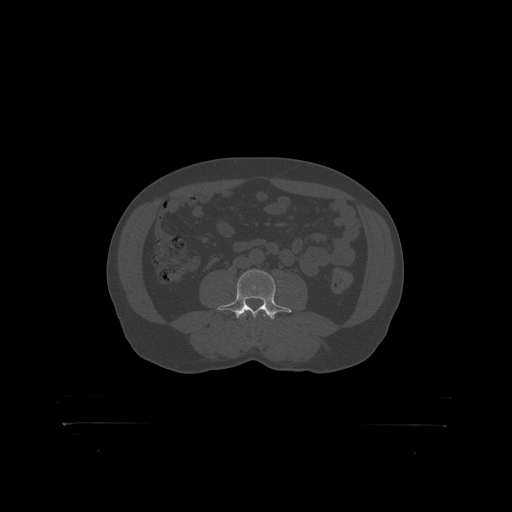
CT including the spine, one axial slice. Position 242 of 399 along the scan axis. Reconstruction kernel STANDARD. Bone window (W 1800 / L 400 HU). 1.25 mm slice thickness. 512 × 512 image matrix, field of view 650 × 650 mm. Male patient, age 46 years. Case-level facts recorded for this patient, not image findings: primary cancer: skin.
Outlined on this slice (semi-automatically segmented with operator editing):
- L3 vertebra: bounding box (x1, y1, x2, y2) in pixels: (245, 314, 265, 316)
- L4 vertebra: (220, 270, 289, 319)